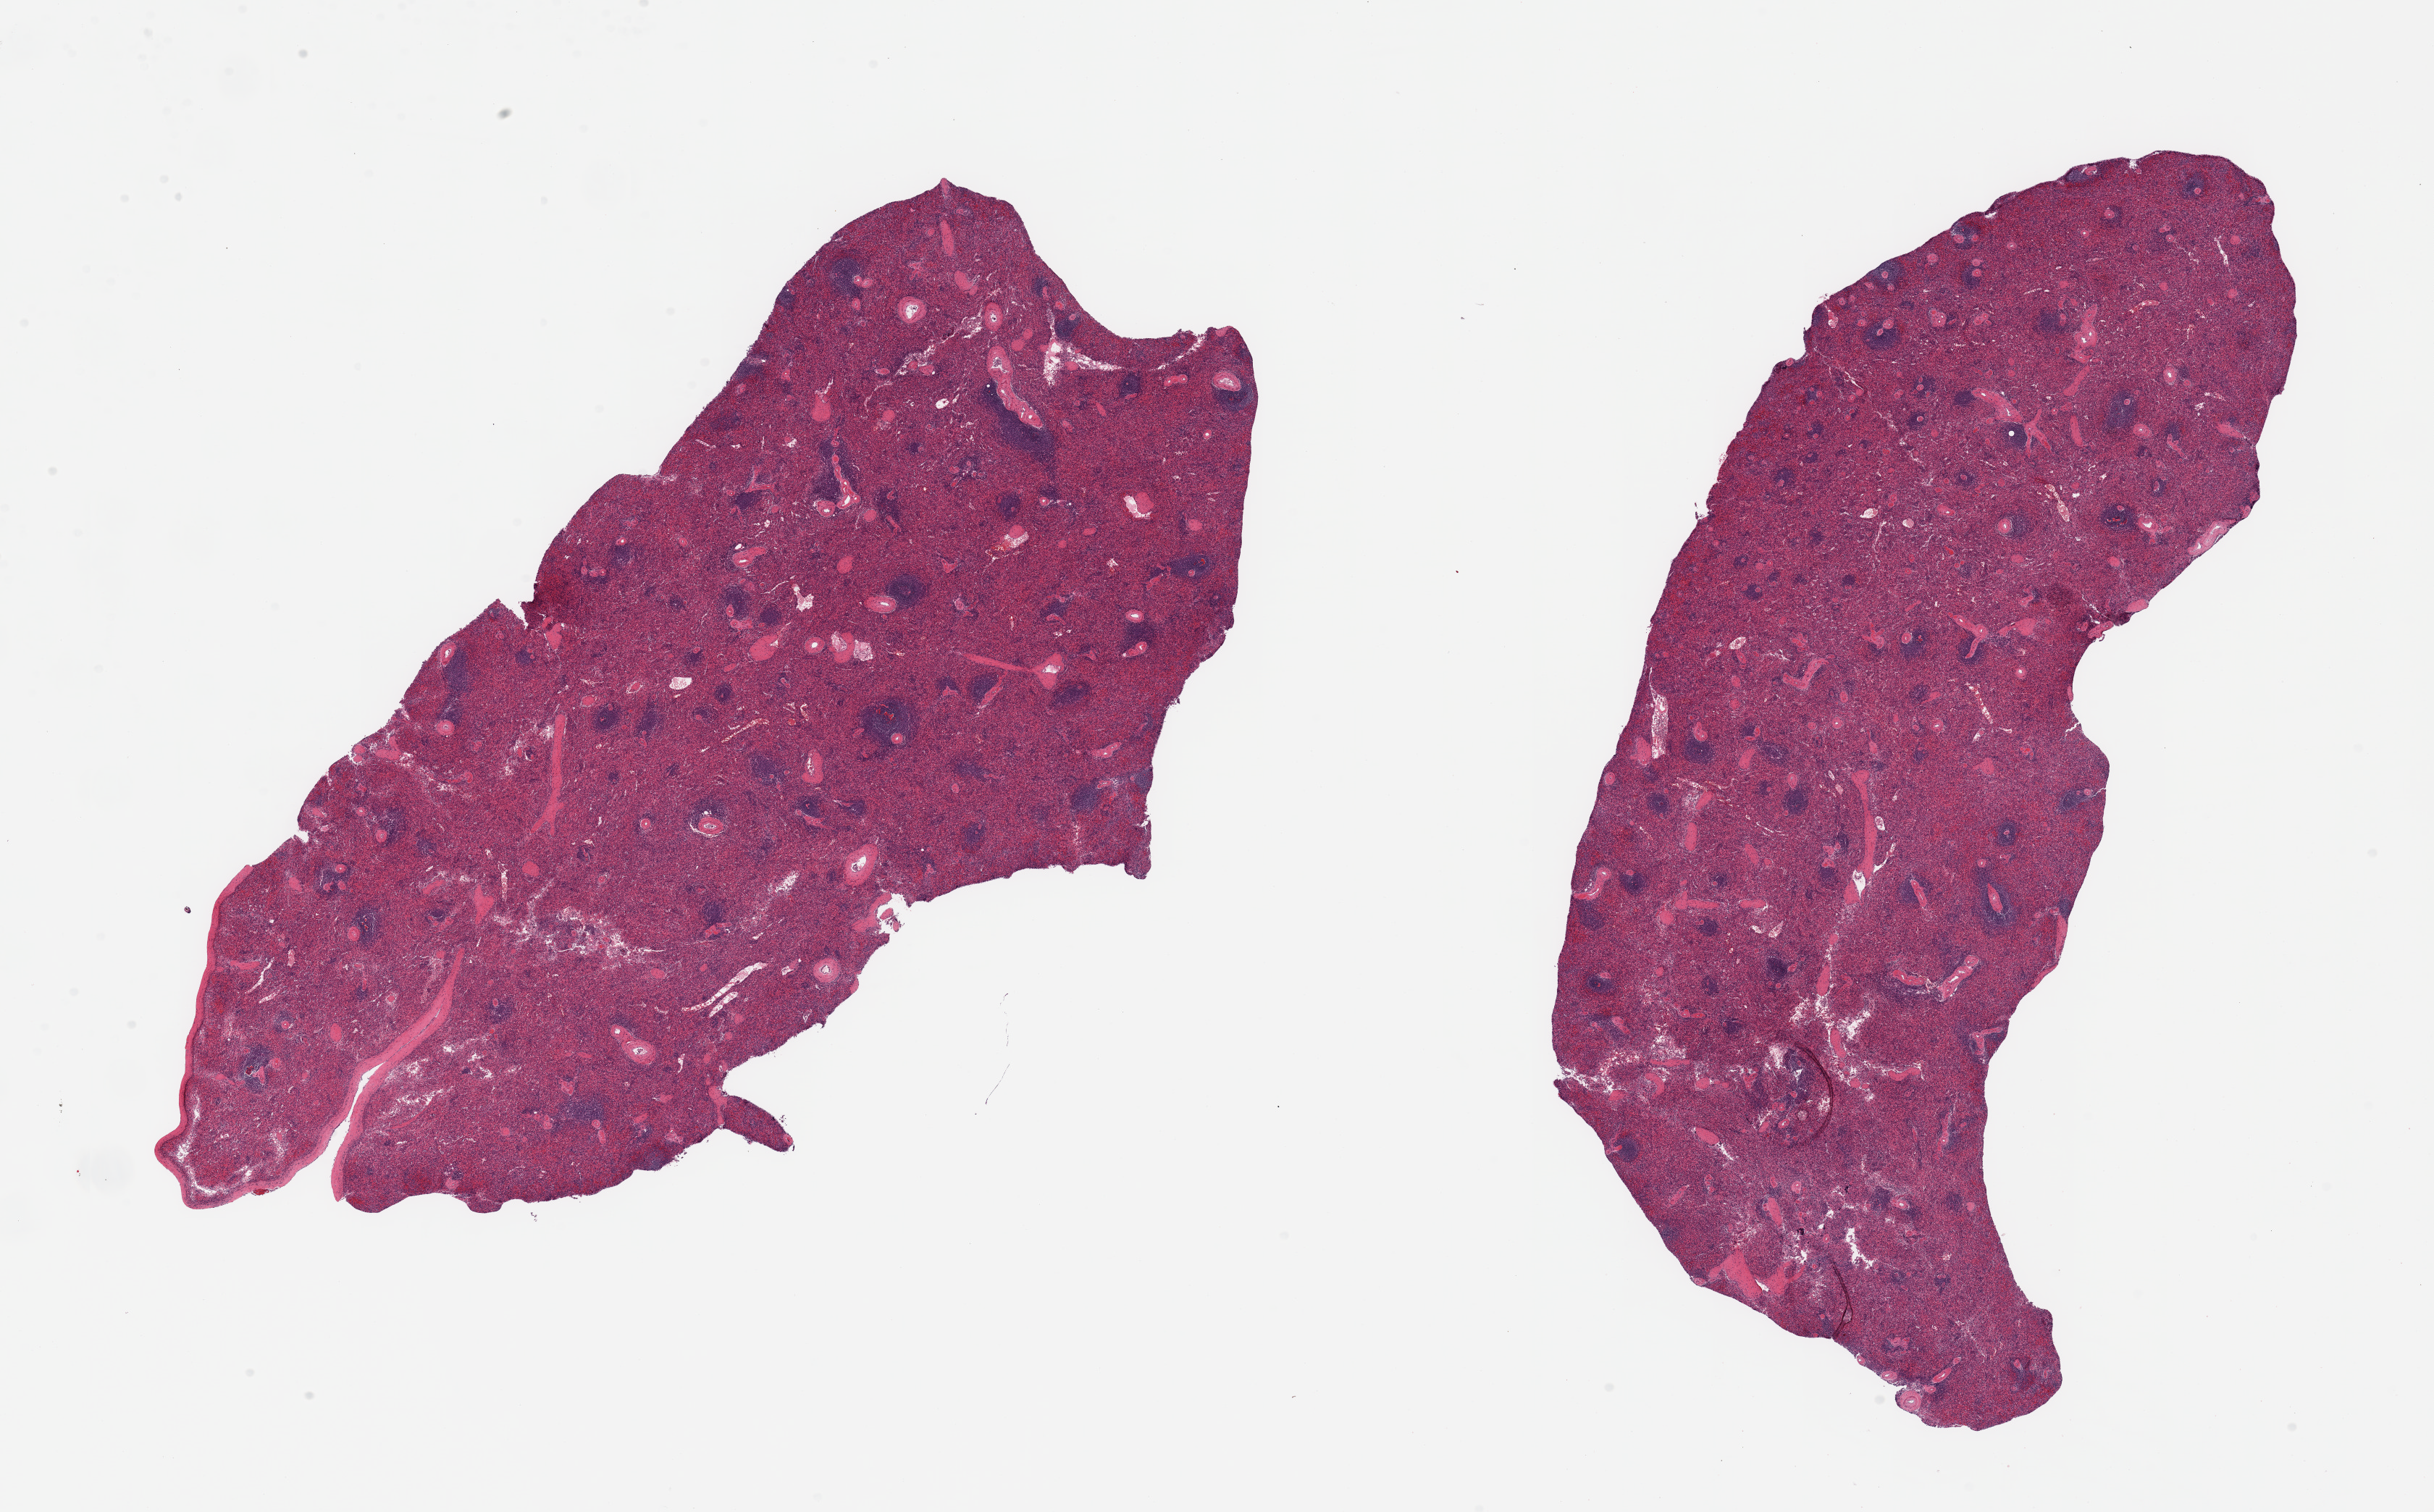
Digitized H&E-stained section, low-resolution overview of the scanned area, about 26.6 x 16.5 mm; PAXgene-fixed, paraffin-embedded tissue; section of spleen (target tissue); donor tissue sample. Donor sex: female.
Pathologist's review note for this sample: 2 pieces; 1 piece includes portion of capsule.